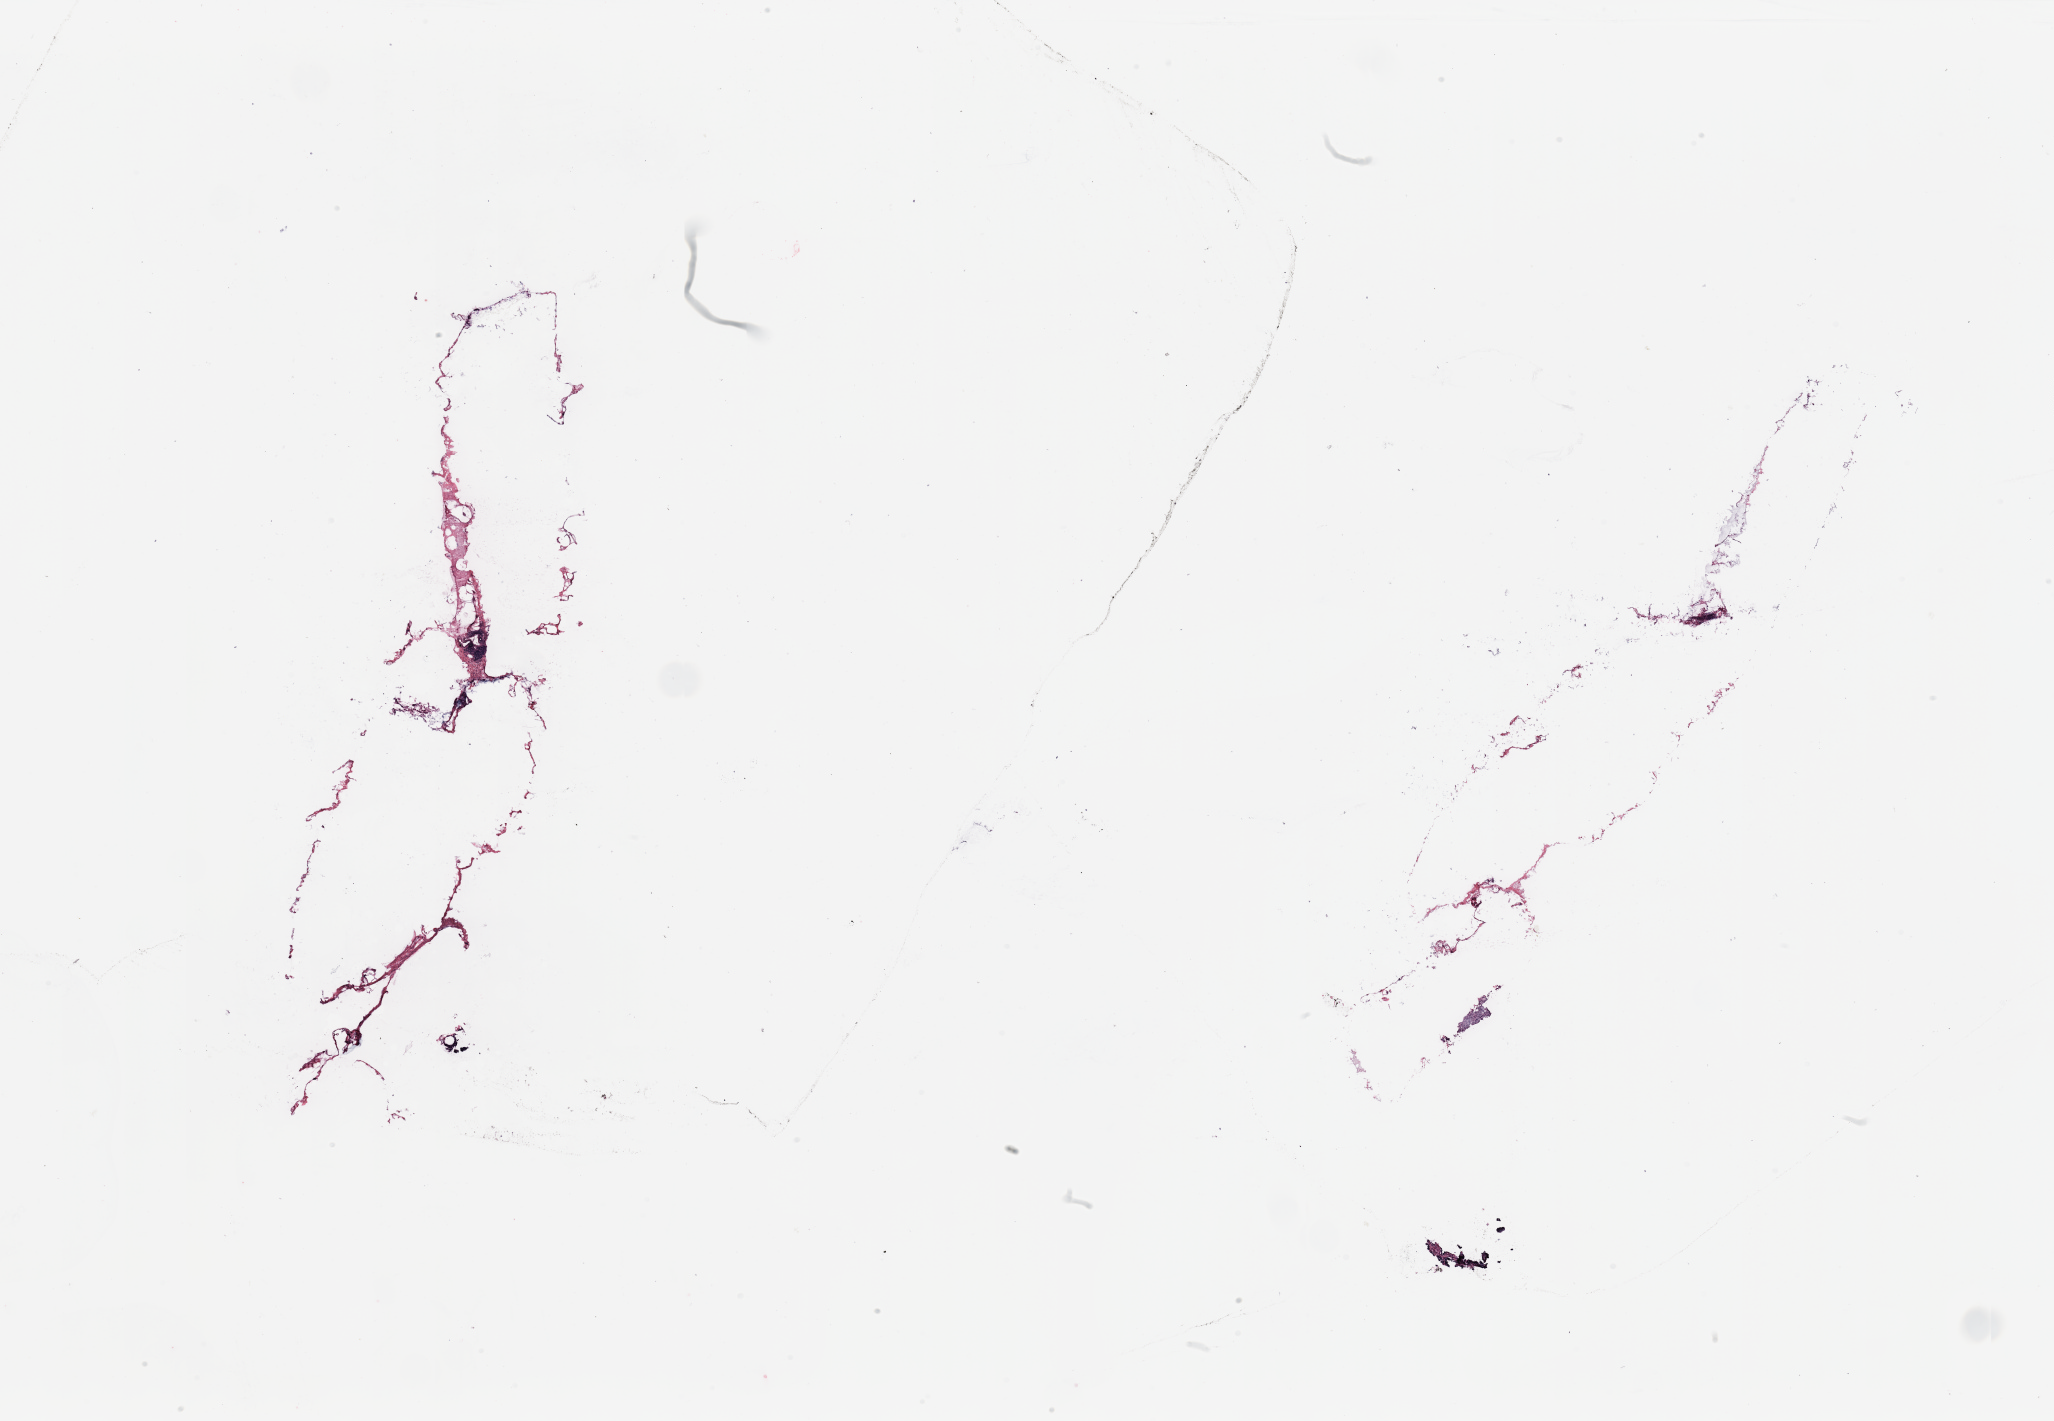
Digitized Hematoxylin and eosin (H&E) stained tissue section (whole slide), whole scanned area (about 32.5 x 22.5 mm, from a 20x scan) shown as a low-resolution overview; breast, tumour tissue. Female, 80 y/o.
Diagnosis: Infiltrating duct carcinoma, NOS. AJCC pathologic stage: IIA.